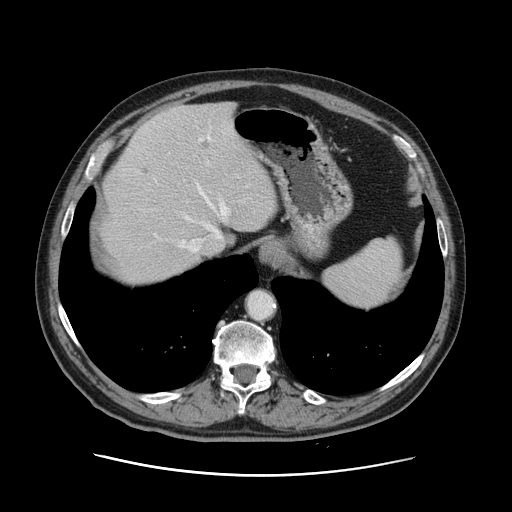
Contrast-enhanced abdominal CT, one axial slice; slice 104 of 141 in the series (ordered by position); 120 kVp; intravenous contrast given; soft-tissue window (W 400 / L 40 HU); 2.5 mm slice thickness; 512 × 512 image matrix. Male patient, age 72 years. From the clinical record (not read from this slice): diagnosis: colorectal cancer liver metastases, imaged before liver resection.
Structures marked on this image (expert manual segmentation):
- hepatic veins: bounding box [x1, y1, x2, y2] px = [155, 137, 227, 252]
- liver: [100, 102, 277, 288]
- planned liver remnant (the part of the liver to remain after resection): [117, 102, 277, 288]
- portal vein (with intrahepatic branches): [199, 138, 227, 213]